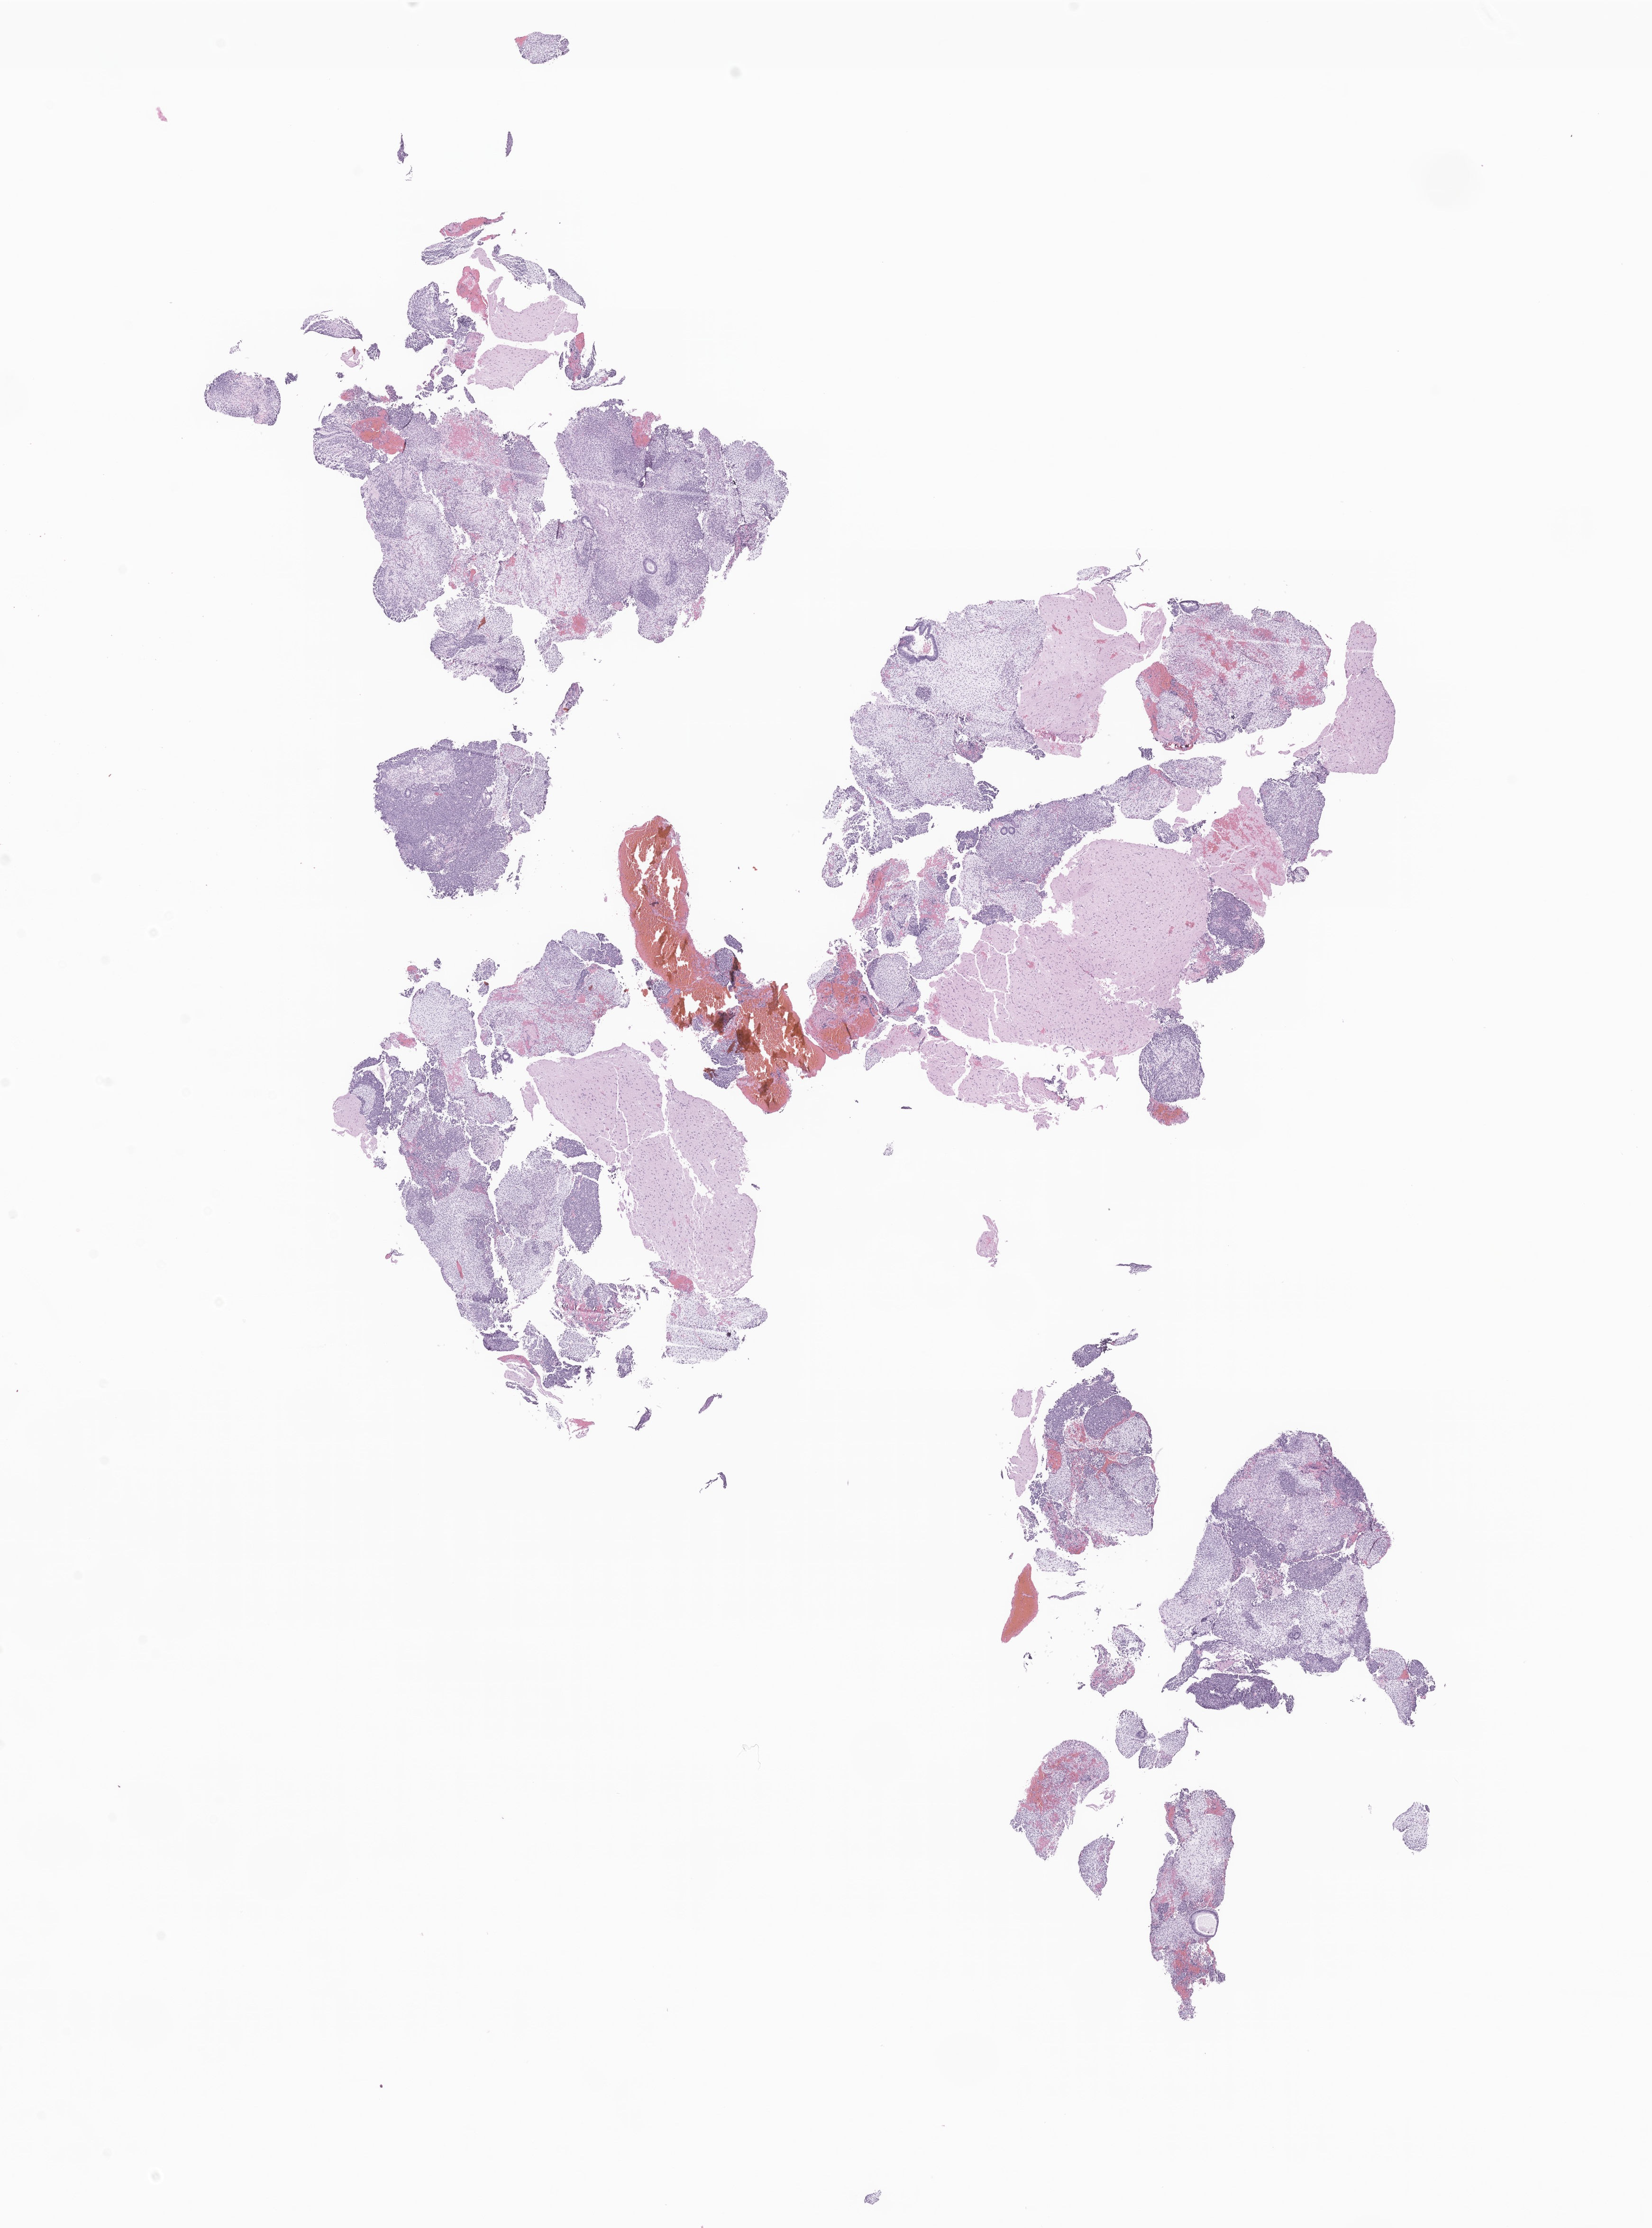
H&E whole-slide image of tumor tissue from the brain, shown as a low-resolution overview of the whole scanned area (about 14.7 x 19.8 mm). Formalin-fixed, paraffin-embedded (FFPE) tissue. Patient female; age 141 days.
Diagnosis: Atypical teratoid/rhabdoid tumor.